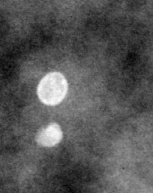
Crop from a digitized film mammogram around one marked abnormality, right breast, MLO view.
- Finding: calcifications, morphology round and regular / eggshell; BI-RADS assessment category 2; benign without callback (not worked up further).